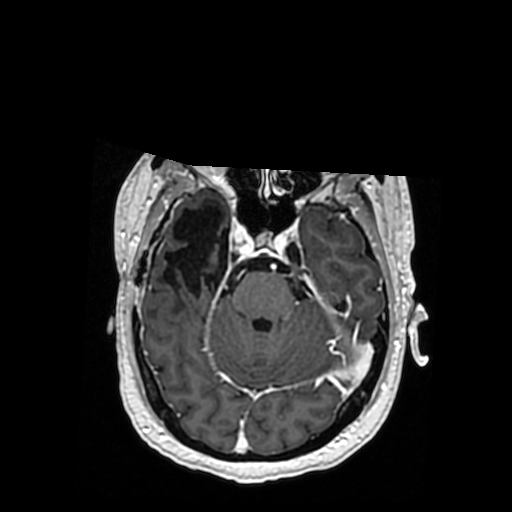
Brain MRI from a brain-tumour surgery series, one axial slice. Position 238 of 364 along the scan axis. T1-weighted post-contrast. 0.5 mm slice thickness. 512 × 512 image matrix. Case-level facts recorded for this patient, not image findings: histopathology: Oligodendroglioma; WHO grade: 3.
Structures marked on this image (manually delineated by an expert):
- previous resection cavity: bounding box <164,206,229,297> (left, top, right, bottom; pixels)